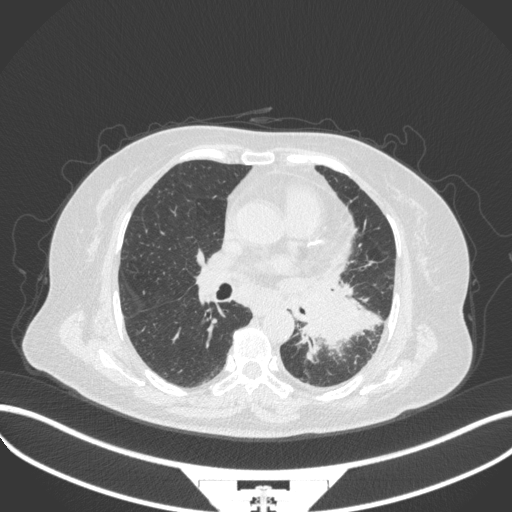
Chest CT, one axial slice. Position 182 of 328 along the scan axis. Lung window (W 1500 / L -600 HU). 1 mm slice thickness. 512 × 512 image matrix, field of view 400 × 400 mm. Female patient, age 69 years. From the clinical record (not read from this slice): clinical TNM (as recorded): T2b N3 M1.
Outlined on this slice (rectangle marked by the reading radiologist):
- lung tumour (recorded histology: adenocarcinoma): bounding box <295,283,390,359> (left, top, right, bottom; pixels)